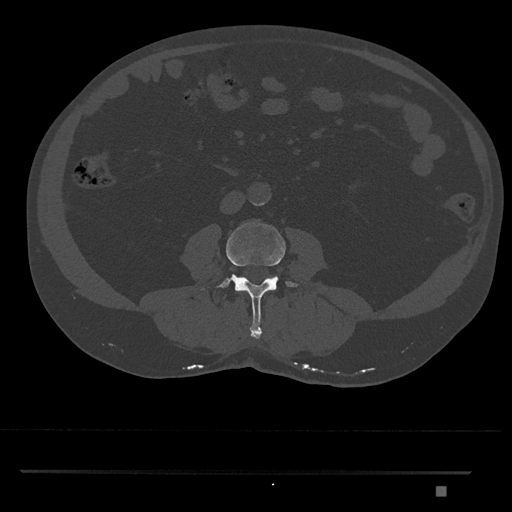
CT including the spine, one axial slice. Position 675 of 1134 along the scan axis. Bone window (W 1800 / L 400 HU). 0.5 mm slice thickness. 512 × 512 image matrix, field of view 429 × 429 mm. Patient: male, 65 years. From the clinical record (not read from this slice): primary cancer: prostate.
Annotated regions visible in this slice (semi-automatic segmentation, software-assisted and operator-edited):
- L3 vertebra: bounding box [x1, y1, x2, y2] px = [201, 222, 300, 339]